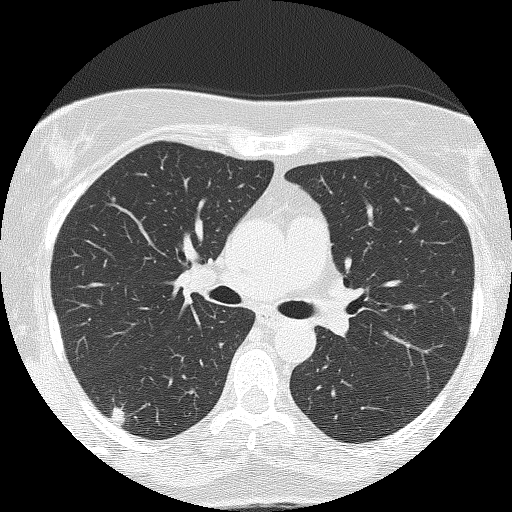
Low-dose screening chest CT, one axial slice. Slice 86 of 143 in the series (ordered by position). Reconstruction kernel FC51. 120 kVp. Lung window (W 1500 / L -600 HU). 2 mm slice thickness. 512 × 512 image matrix, field of view 301 × 301 mm.
Annotated regions visible in this slice (outlined manually by an expert reader):
- lesion 1 (tumor, lower lobe of right lung): bounding box [x1, y1, x2, y2] px = [111, 407, 125, 425]